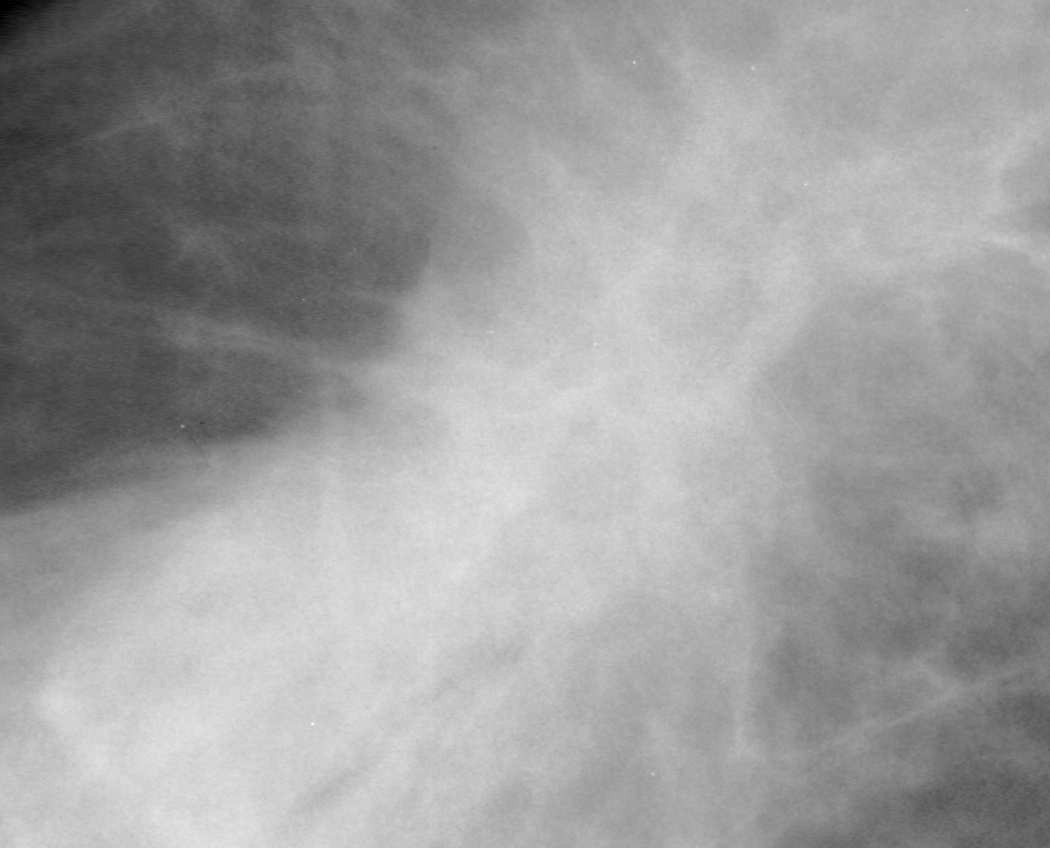
Region of interest cut from a scanned film mammogram (one marked finding), left breast, CC view, BI-RADS breast density category 4 (scale 1–4).
Marked abnormality: mass, shape architectural distortion, margins spiculated; BI-RADS assessment category 2; subtlety rating 5 on a 1 (subtle) to 5 (obvious) scale; benign; no additional work-up was recommended (benign without callback).